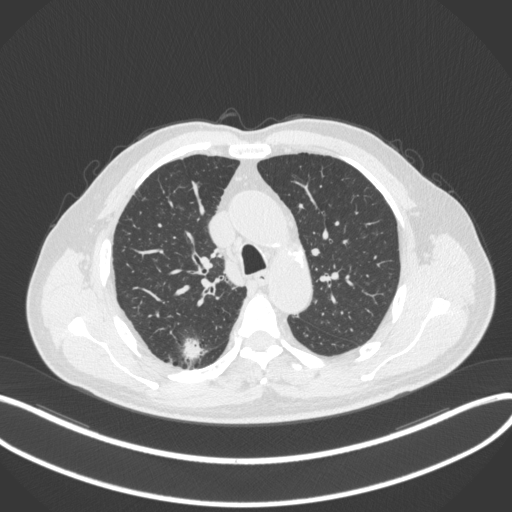
Chest CT, one axial slice. Position 263 of 366 along the scan axis. Reconstruction kernel B31f. 120 kVp. Lung window (W 1500 / L -600 HU). 1 mm slice thickness. 512 × 512 image matrix. Male patient, age 69 years. Case-level facts recorded for this patient, not image findings: clinical TNM (as recorded): T1b N0 M0; histopathological grade: G2-3.
Structures marked on this image (rectangle marked by the reading radiologist):
- lung tumour (recorded histology: adenocarcinoma): box from (x=178, y=333) to (x=206, y=363) px